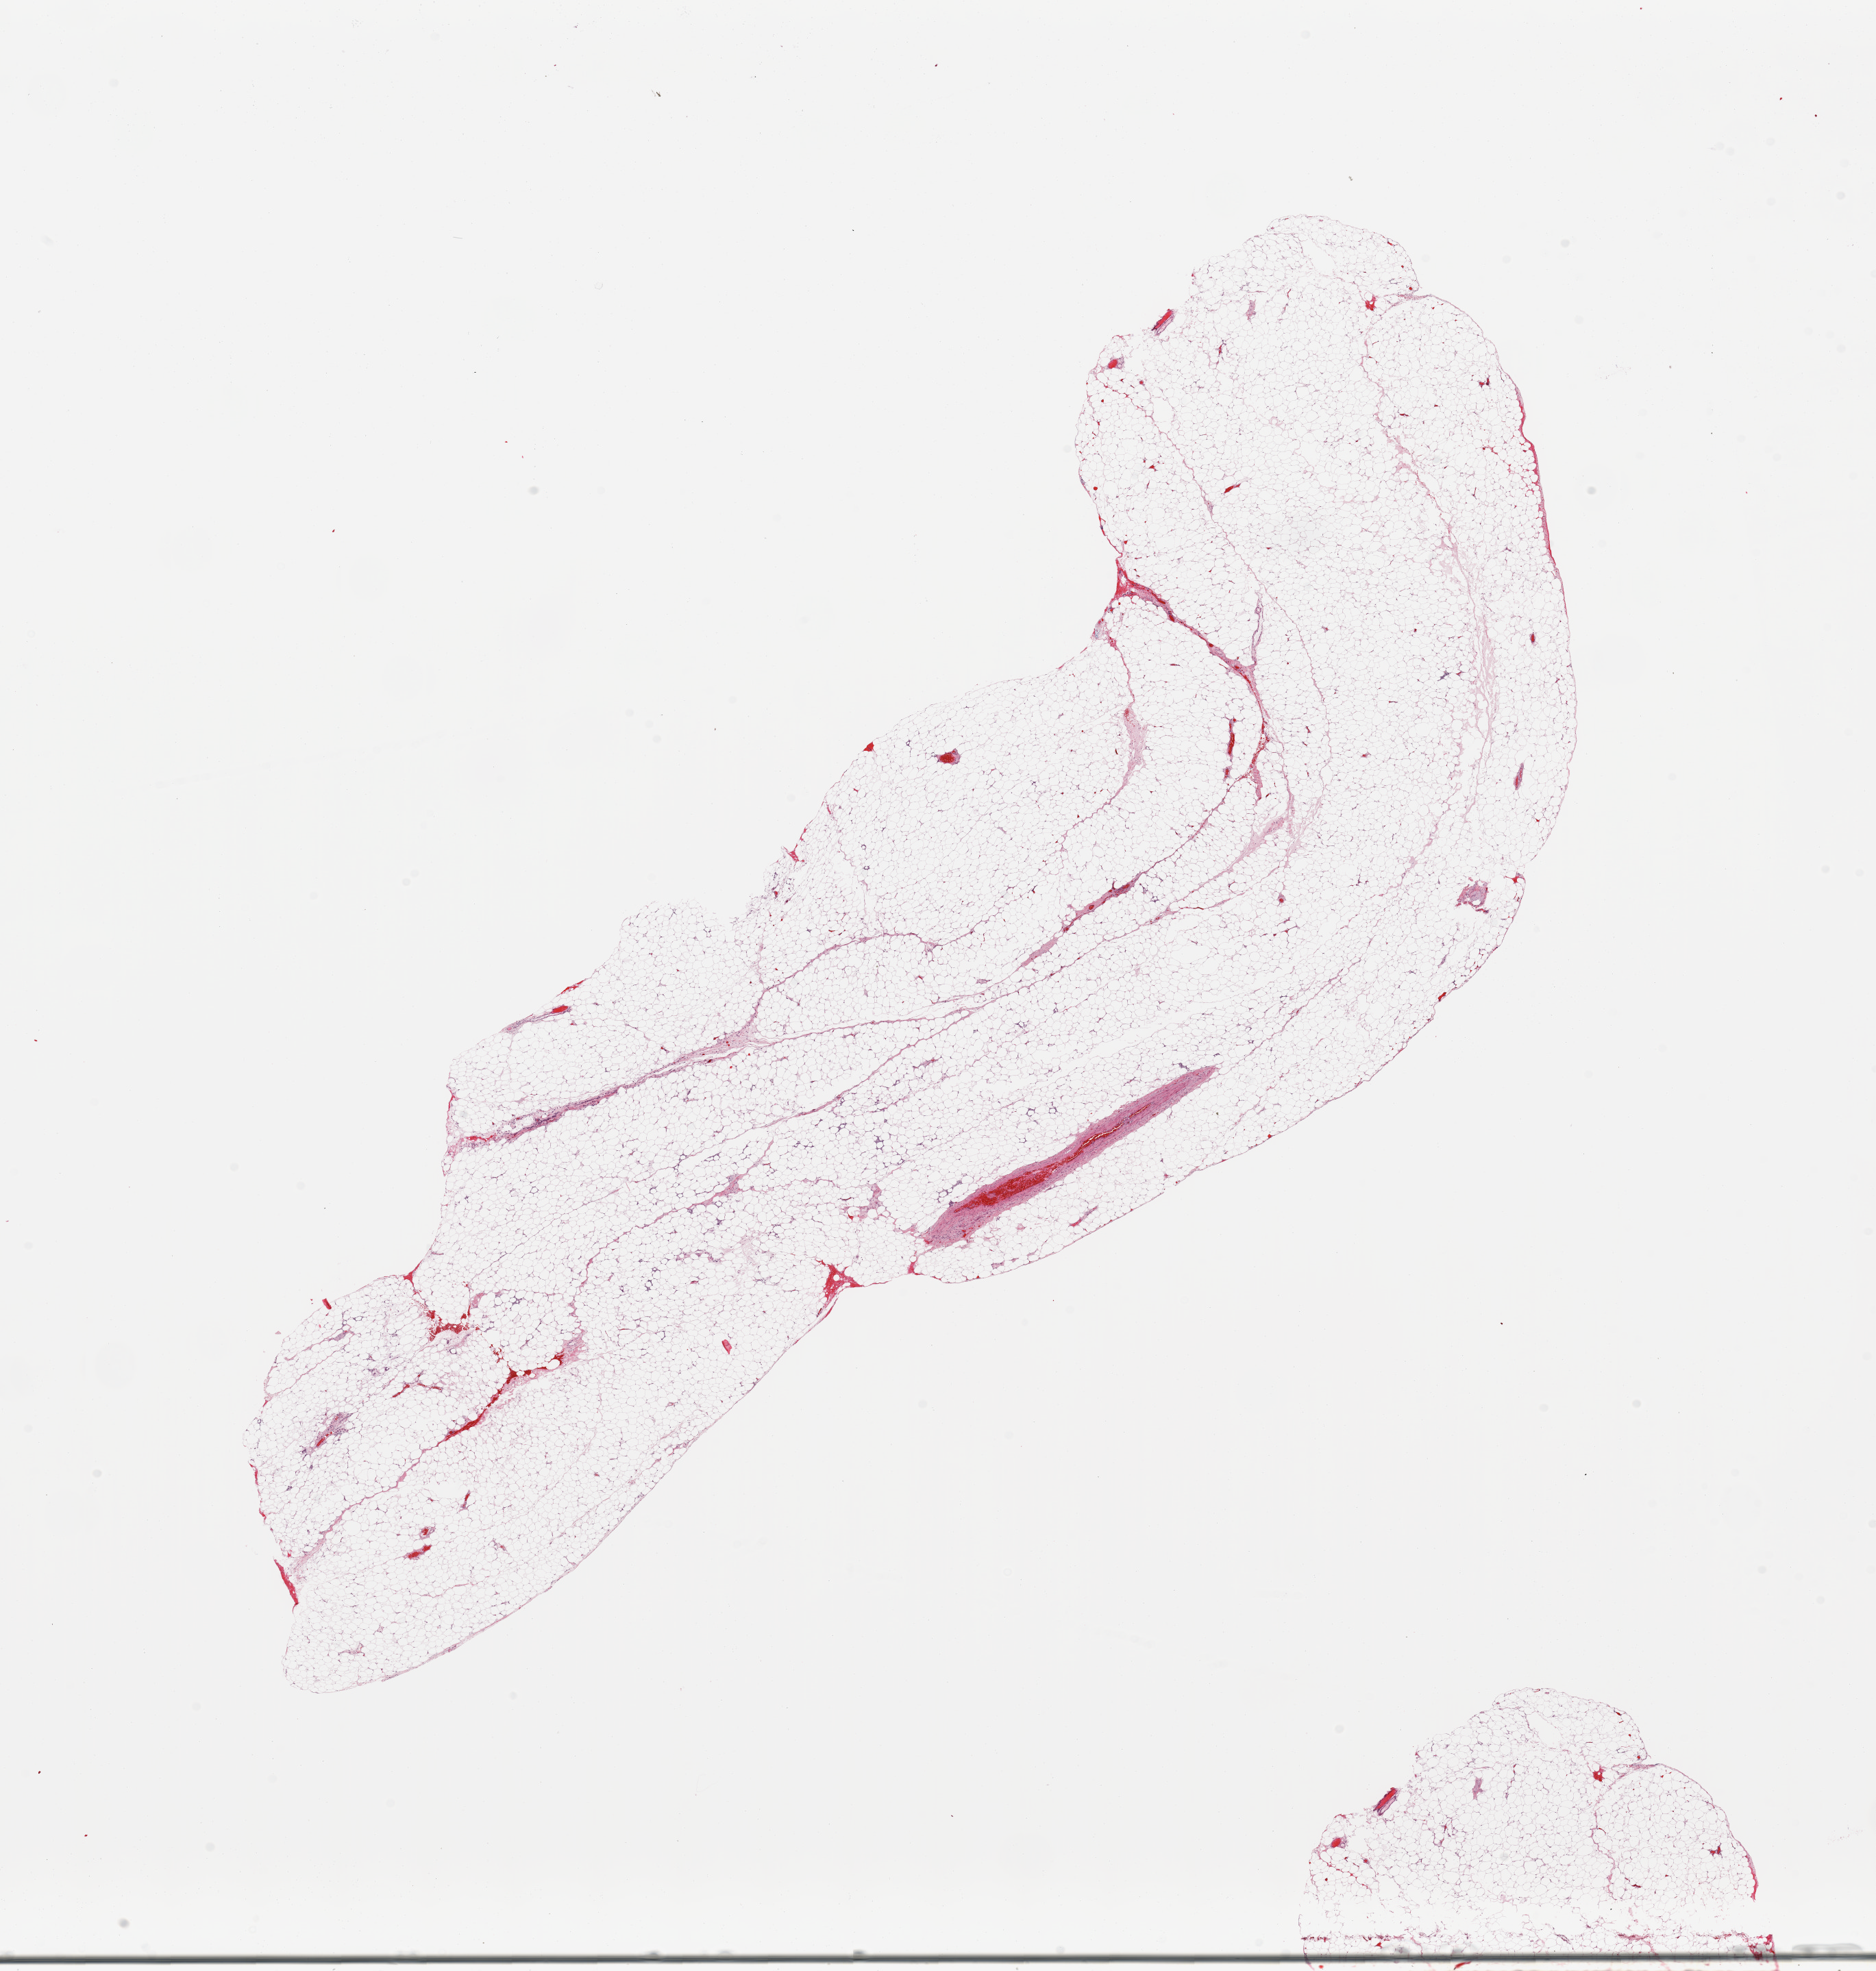
H&E-stained whole-slide image, low-resolution overview of the scanned area, about 21.7 x 22.8 mm. Normal (non-tumour) tissue sample. Male patient.
This section: normal (non-tumour) tissue from the same patient. Patient diagnosis (cohort enrolment): sarcoma (site not recorded at cohort level).